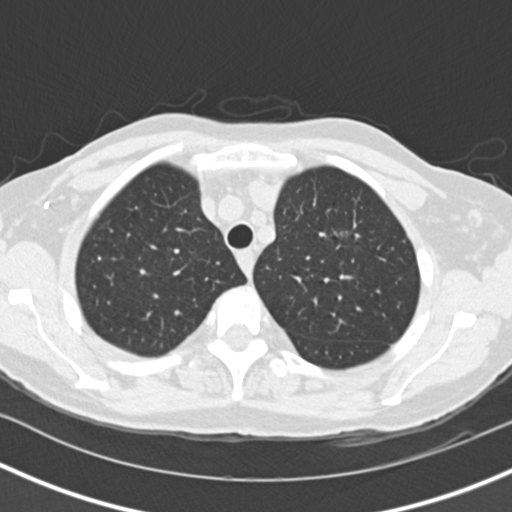
Axial slice from a low-dose chest CT screening exam. First (baseline) screen. Lung window (W 1500 / L -600 HU). 2 mm slice thickness. Slice 29 of 146 in the series. 512 × 512 image matrix, field of view 310 × 310 mm. Female participant, aged 73 years at enrolment. Current smoker at enrolment.
- Expert reader's lesion annotation, bounding box <315,210,370,277> (left, top, right, bottom; pixels).
- The exam's reader record, not a measurement of the box and not confirmed to be the same lesion: non-calcified nodule or mass ≥4 mm, left upper lobe, 27 × 21 mm, spiculated (stellate) margins, soft tissue attenuation.
- Official screen result: positive, change unspecified: nodule(s) >= 4 mm or enlarging nodule(s), mass(es), or other non-specific abnormalities suspicious for lung cancer.
- Lung cancer was diagnosed 72 days after this screen: bronchiolo-alveolar adenocarcinoma, NOS, left upper lobe, moderately differentiated (G2), stage IIIB (AJCC 6th edition), 17 mm at pathology.